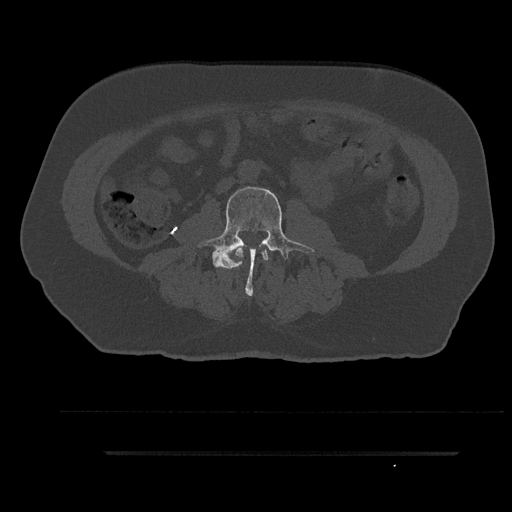
CT including the spine, one axial slice. Reconstruction kernel Br40s/3. 120 kVp. Bone window (W 1800 / L 400 HU). 0.5 mm slice thickness. 512 × 512 image matrix, field of view 432 × 432 mm. Patient: male, 63 years. Case-level facts recorded for this patient, not image findings: primary cancer: renal; vertebrae with lytic lesions (as recorded): T8.
Outlined on this slice (semi-automatically segmented with operator editing):
- L2 vertebra: box from (x=235, y=247) to (x=268, y=267) px
- L3 vertebra: (x=198, y=185)–(x=315, y=296)